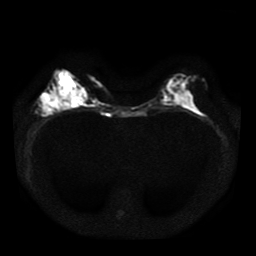
Breast MRI, one axial slice. Diffusion-weighted series; image 2 of 4 stored at this slice position (different b-values; order by instance number). 1.5 T. 256 × 256 image matrix. Female patient.
Annotated regions visible in this slice (outlined manually by an expert reader):
- tumour on diffusion-weighted imaging: bounding box (x1, y1, x2, y2) in pixels: (40, 94, 70, 113)